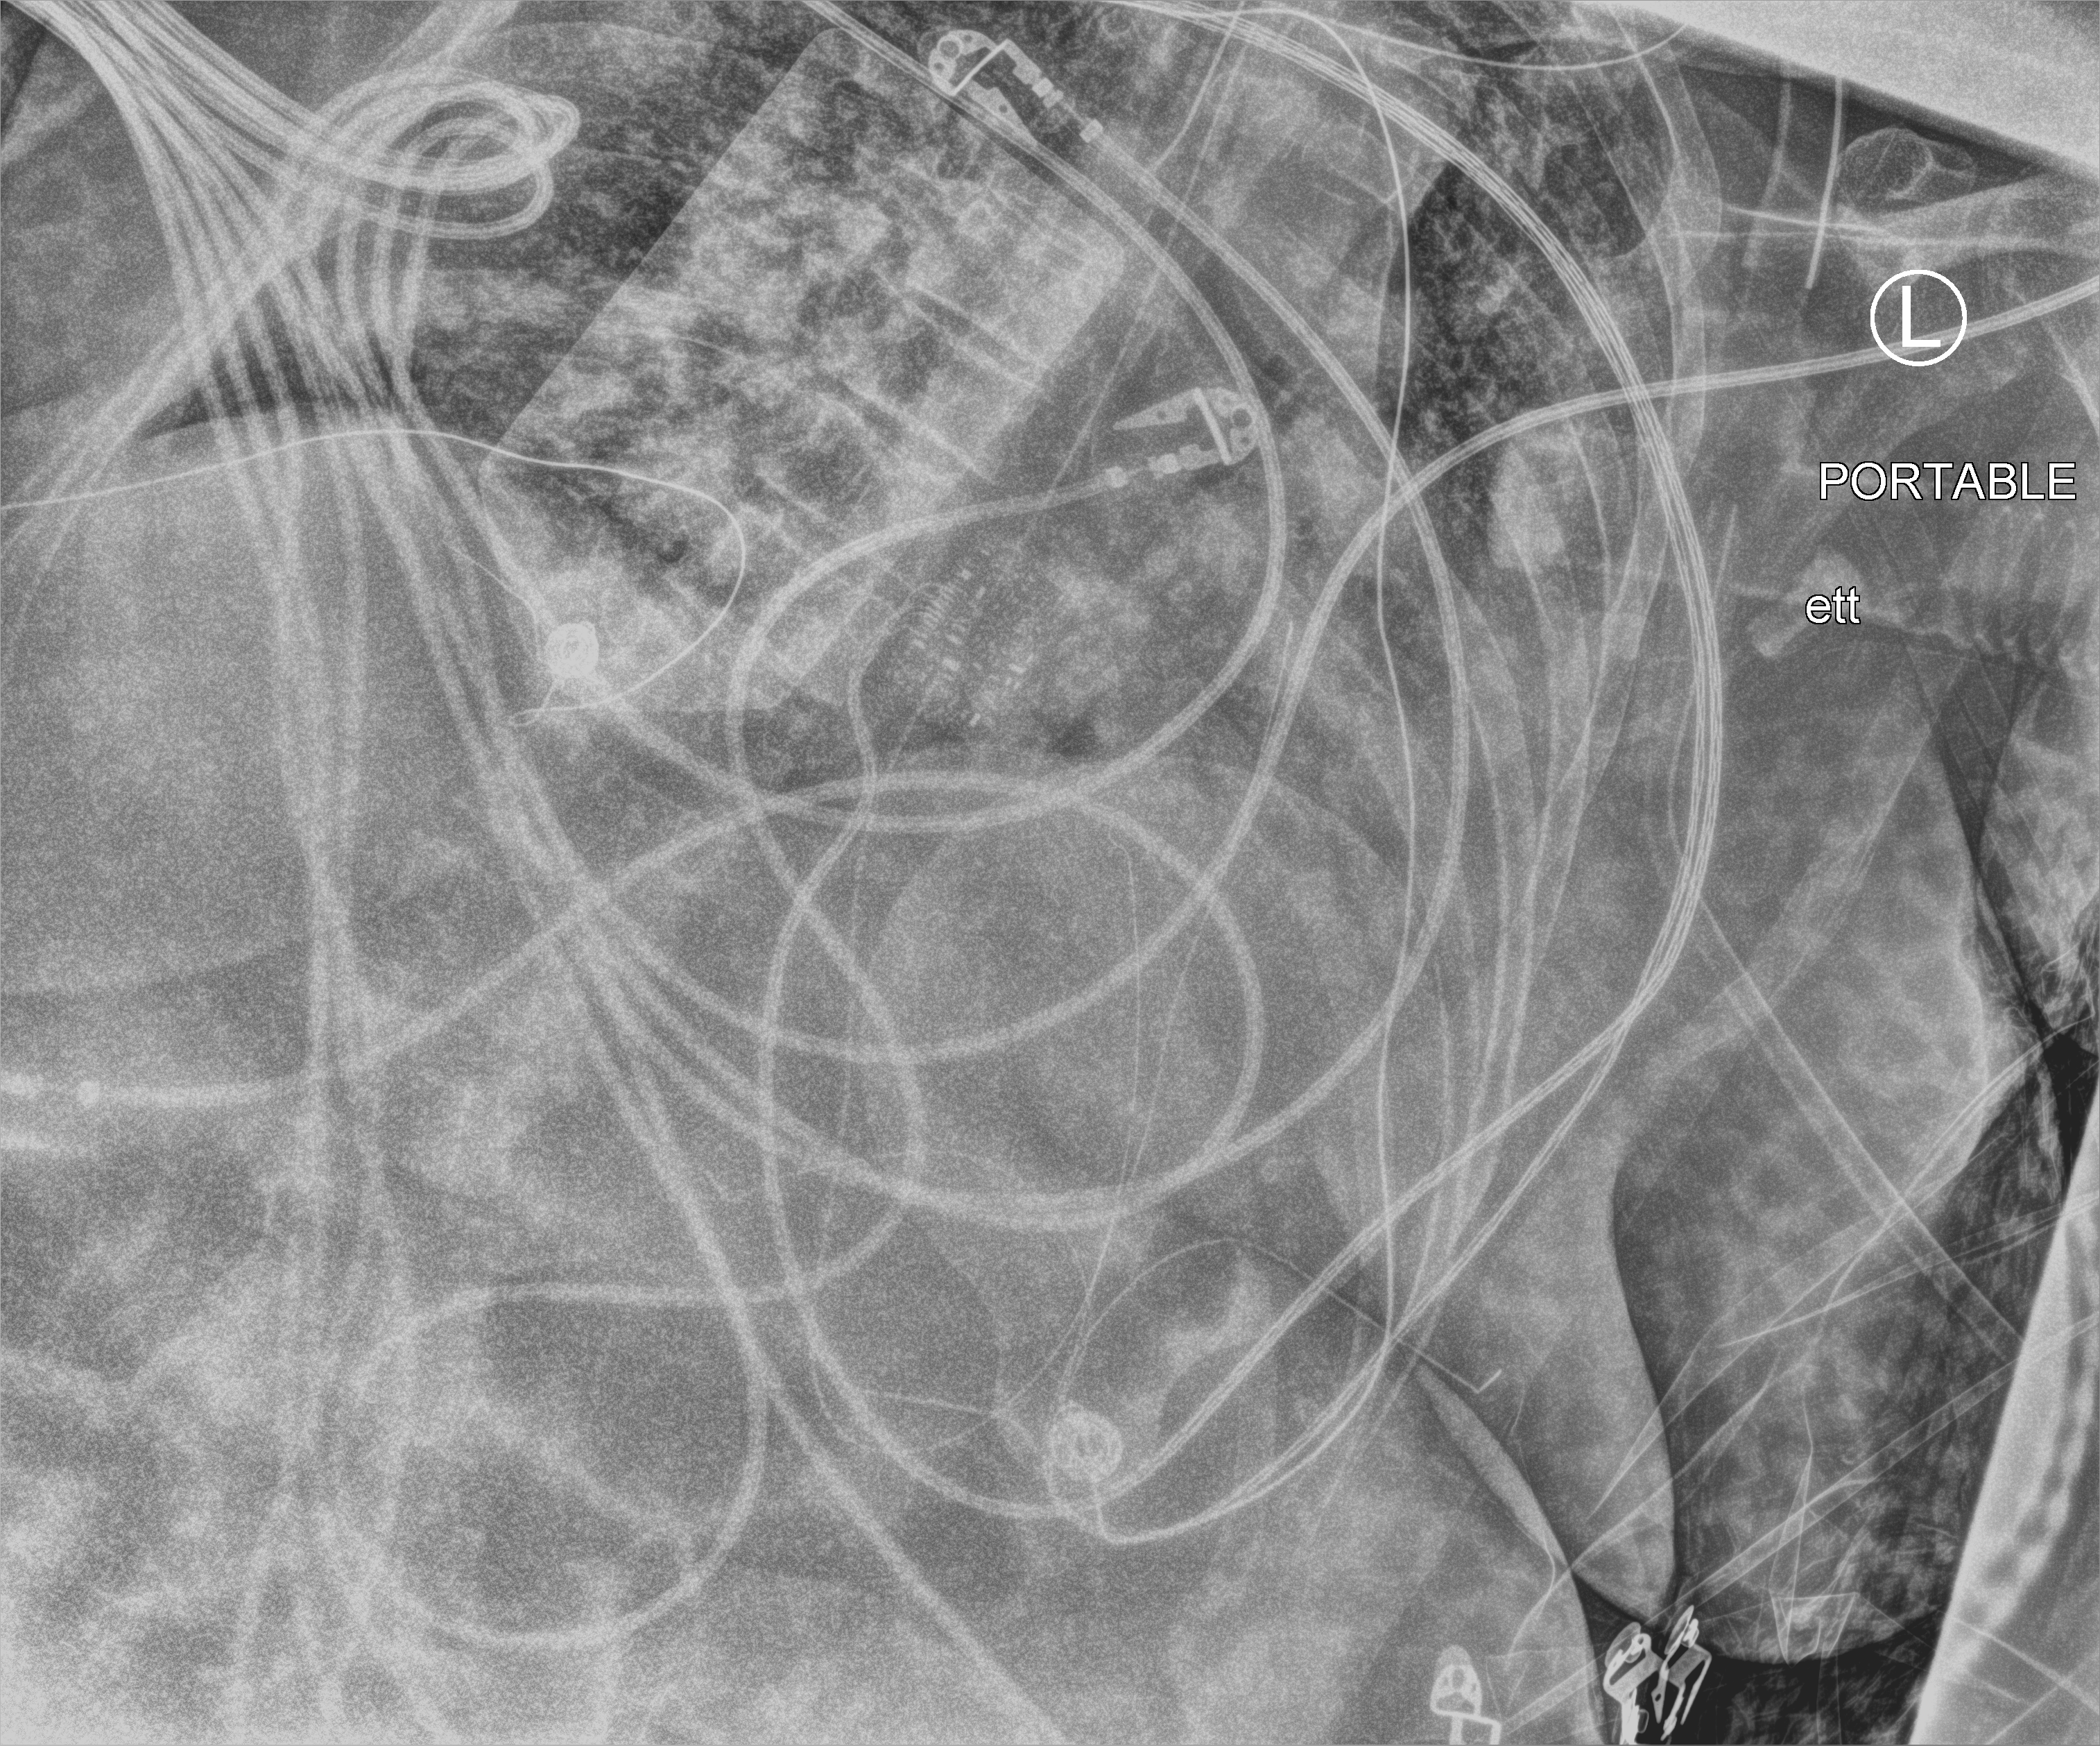
Bedside chest radiograph (computed radiography); anteroposterior (AP) projection. Female patient hospitalised with COVID-19, age 60–74 years.
From the hospital-stay record, not from the radiograph (when in the stay this image was taken is not recorded):
- mechanically ventilated during this hospital stay: yes